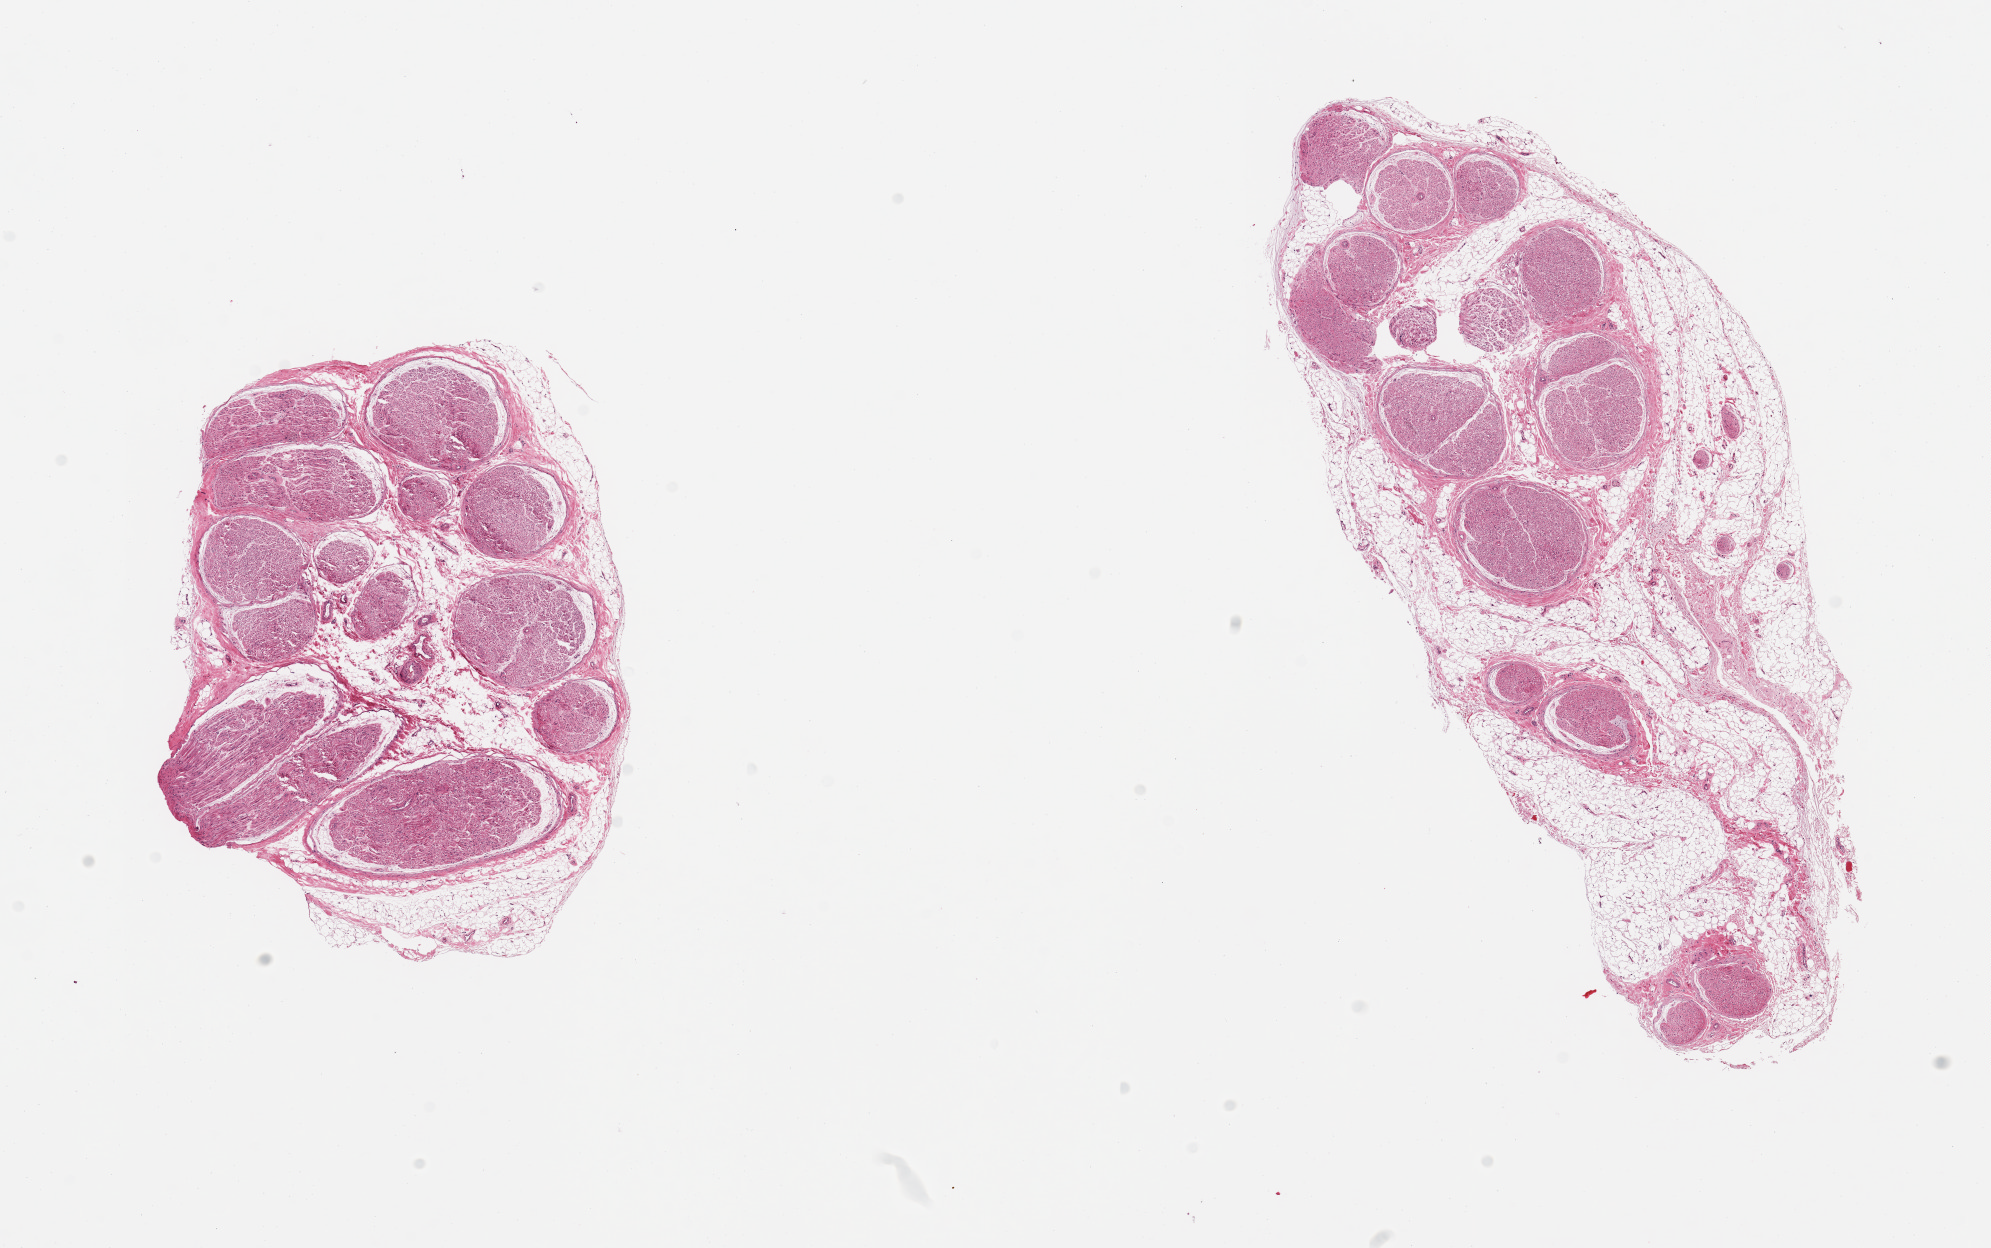
H&E whole-slide image — a low-resolution overview of the entire scanned area, about 15.8 x 9.9 mm, PAXgene-fixed paraffin-embedded (PFPE) section, target tissue: tibial nerve, donor tissue sample. Female donor.
Reviewer comment on this tissue sample: 2 pieces; 20-60% internal and attached fat.